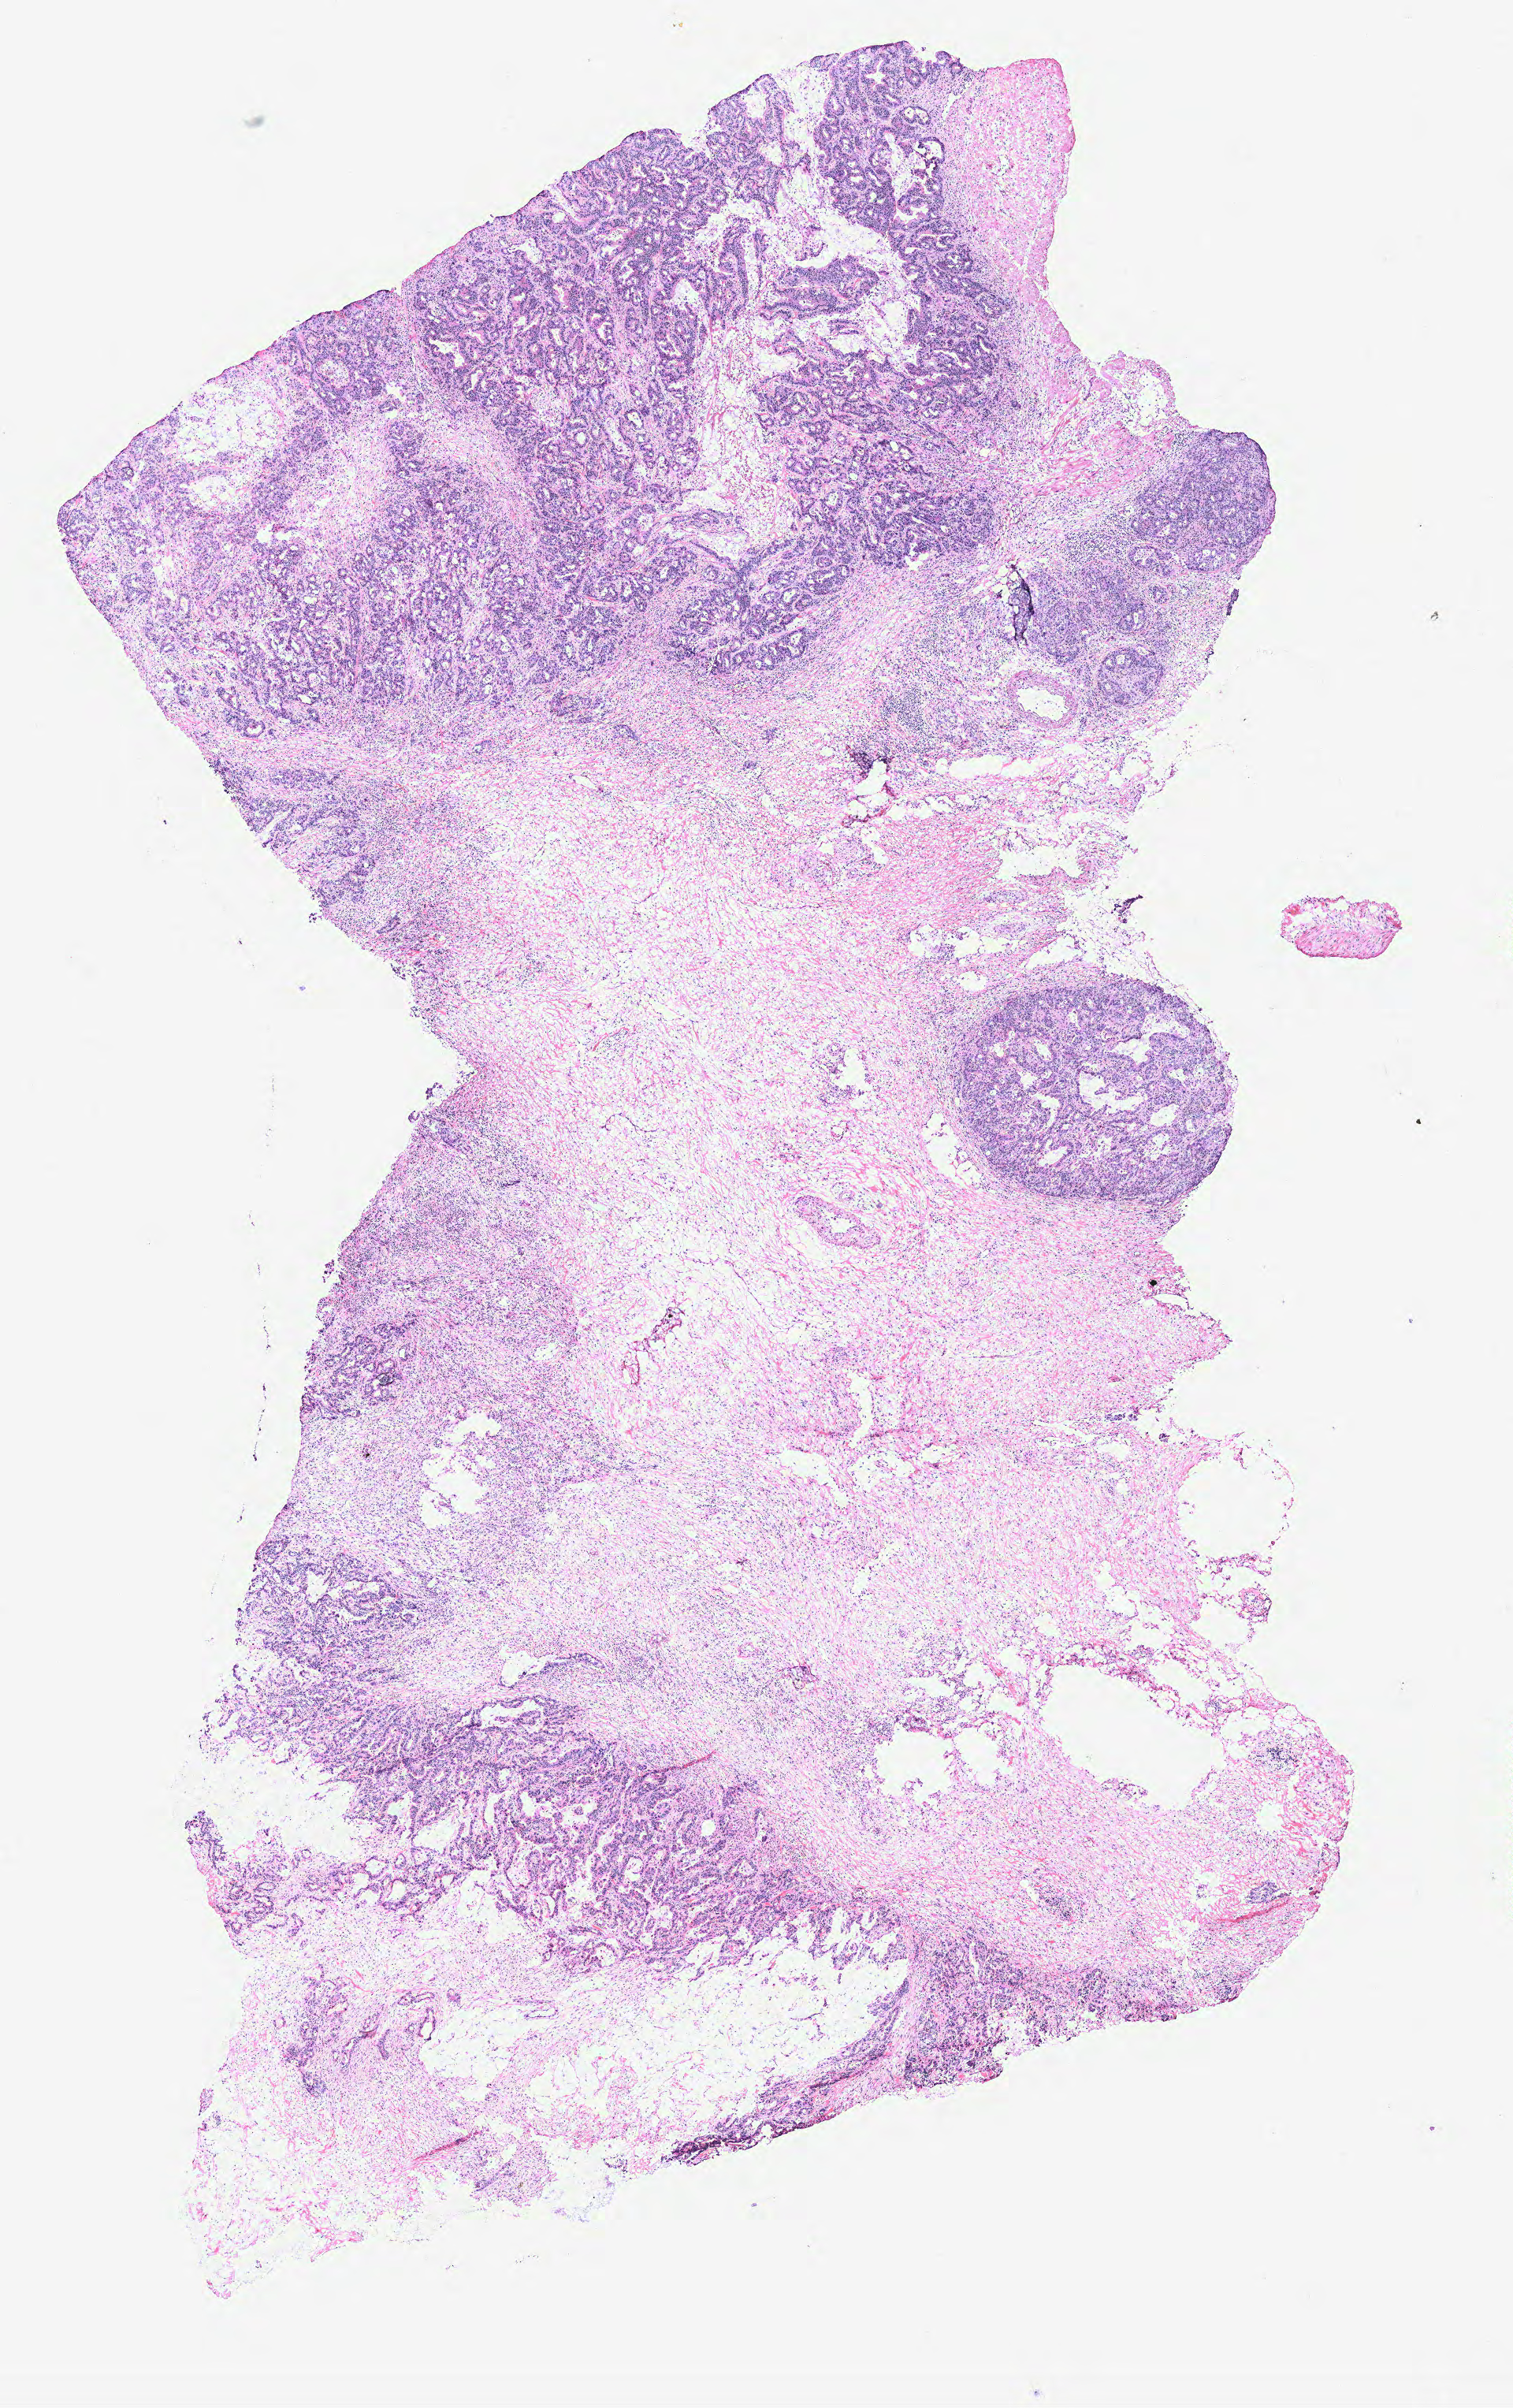
Whole-slide histology image, H&E, low-resolution overview of the scanned area, about 7.7 x 12.2 mm, colon, tissue type not recorded.
Patient diagnosis (cohort enrolment): colon cancer (colon).